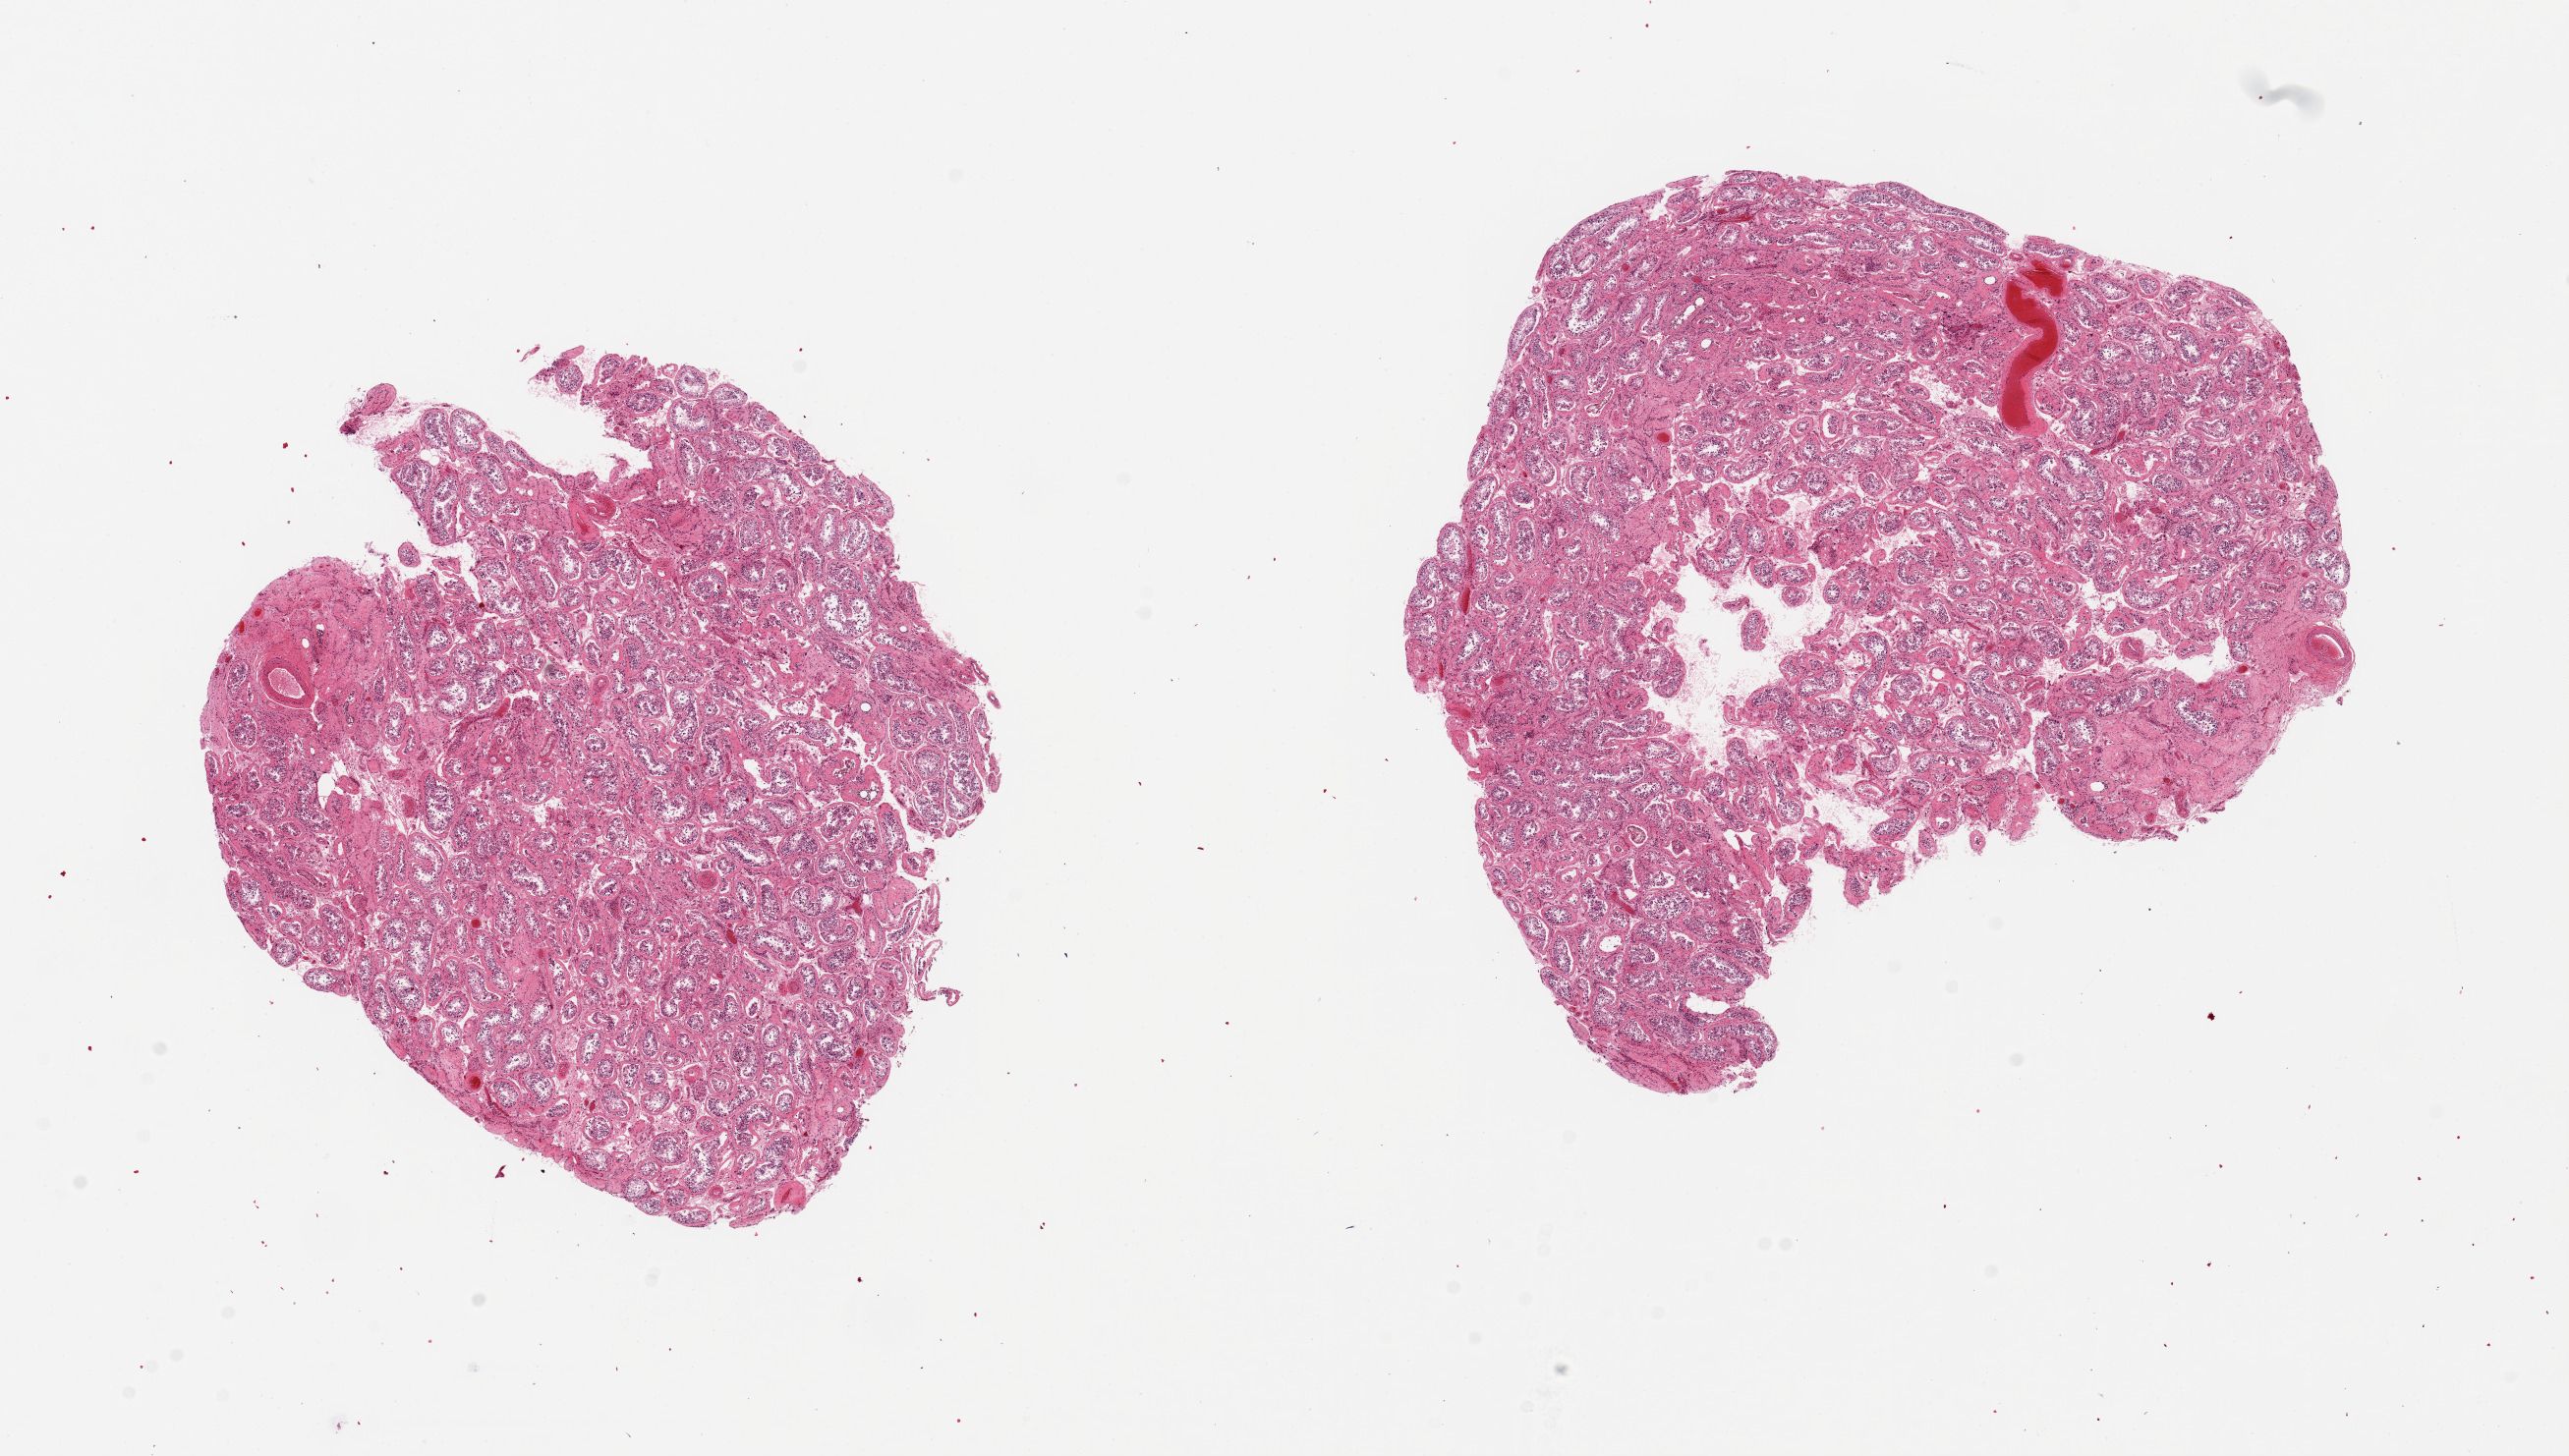
Haematoxylin and eosin whole-slide image, brightfield, a low-resolution overview of the entire scanned area, about 20.7 x 11.7 mm, PAXgene-fixed paraffin-embedded (PFPE) section, target tissue: testis, tissue donor sample. Donor: male.
Reviewer comment on this tissue sample: 2 pieces, 7x6 & 8x7mm; Atrophy, fibrosis, arrested spermatogenesis.